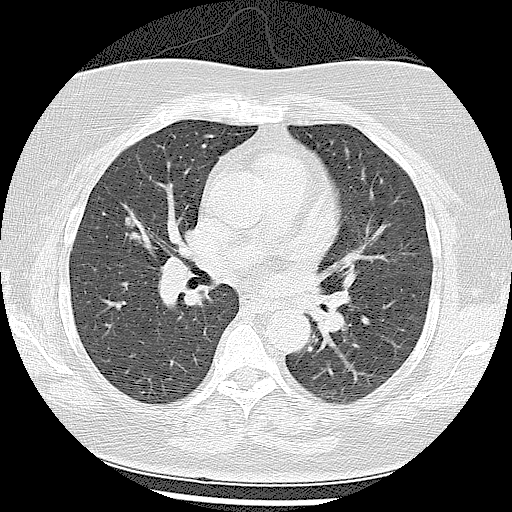
Low-dose screening chest CT, one axial slice. Lung window (W 1500 / L -600 HU). 512 × 512 image matrix.
Structures marked on this image (outlined manually by an expert reader):
- lesion 1 (tumor, middle lobe of right lung): box from (x=125, y=209) to (x=144, y=244) px